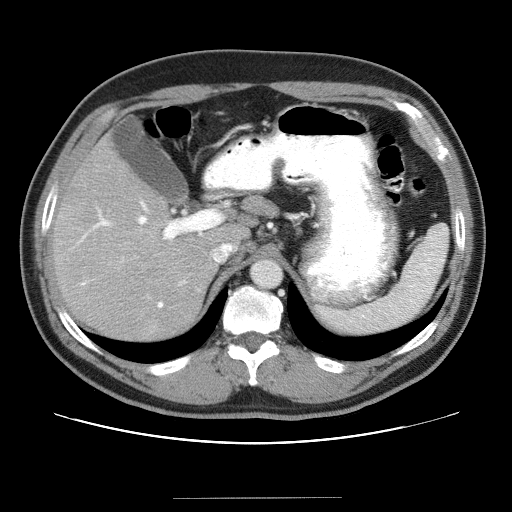
Contrast-enhanced abdominal CT (liver protocol), one axial slice. Position 23 of 40 along the scan axis. 120 kVp. Soft-tissue window (W 400 / L 40 HU). 5 mm slice thickness. 512 × 512 image matrix, field of view 380 × 380 mm. From the clinical record (not read from this slice): diagnosis: hepatocellular carcinoma (patient treated with transarterial chemoembolisation; whether this scan precedes or follows treatment is not stated here); TNM stage (as recorded): Stage-IVA; Child-Pugh class: B; tumour nodularity: multinodular.
Annotated regions visible in this slice (semi-automatically segmented with operator editing):
- liver parenchyma outside the tumour (the mass and vessels are separate outlines, so this box may not span the whole liver): bounding box (x1, y1, x2, y2) in pixels: (52, 134, 252, 340)
- liver vessels: (78, 201, 224, 308)